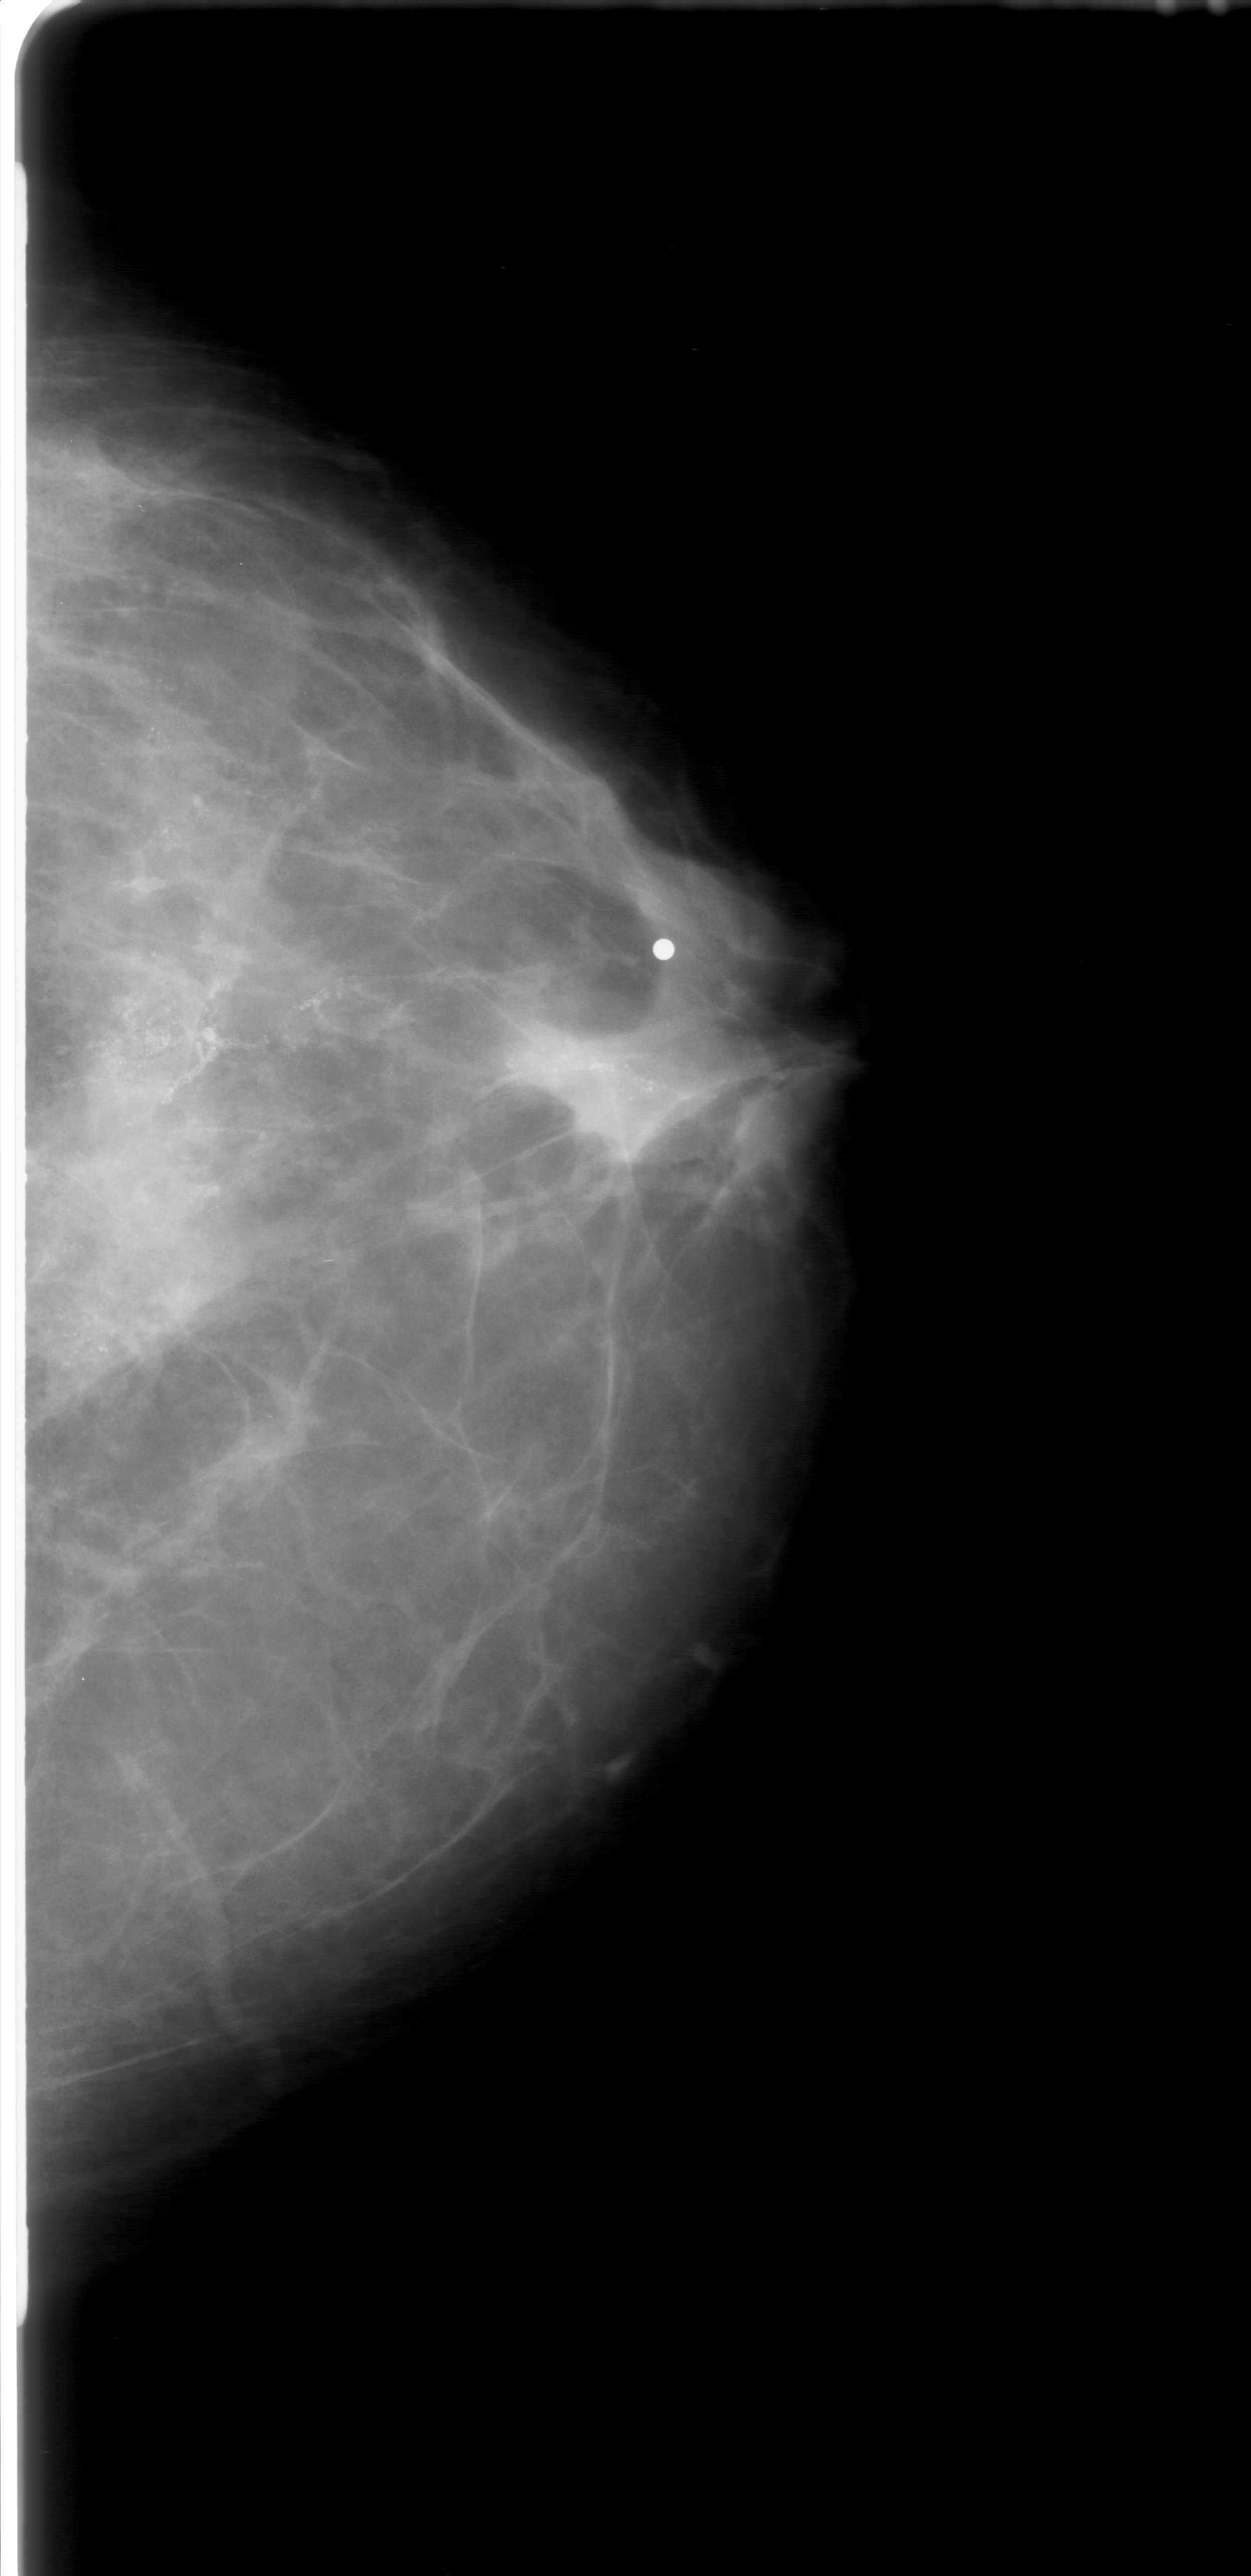
Mammogram (digitized film); left breast; CC view; BI-RADS breast density category 2 (scale 1–4); 1251 × 2576 image matrix.
Expert-marked regions of interest on this image (one box per marked abnormality):
- calcifications, morphology amorphous, distribution linear; BI-RADS assessment category 5; subtlety rating 5 on a 1 (subtle) to 5 (obvious) scale; pathology result (as recorded, not read from the image): malignant: box from (x=37, y=613) to (x=701, y=1490) px